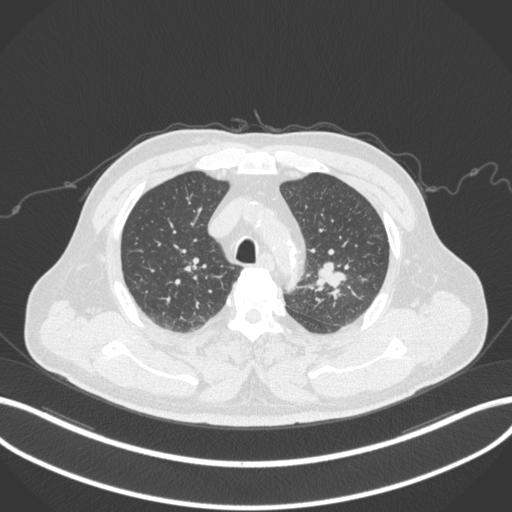
Chest CT, one axial slice. Slice 233 of 286 in the series (ordered by position). Reconstruction kernel B31f. Lung window (W 1500 / L -600 HU). 1 mm slice thickness. 512 × 512 image matrix, field of view 400 × 400 mm. Male patient, age 67 years. From the clinical record (not read from this slice): clinical TNM (as recorded): T2a N1 M0; histopathological grade: G3.
Outlined on this slice (bounding box drawn by a radiologist):
- lung tumour (recorded histology: adenocarcinoma): bounding box [x1, y1, x2, y2] px = [311, 257, 350, 294]